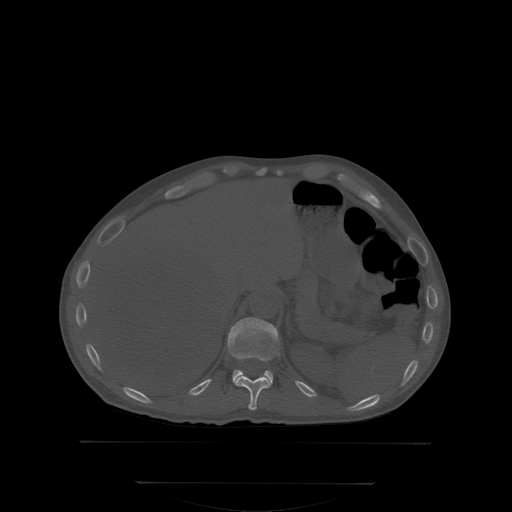
CT including the spine, one axial slice; slice 176 of 350 in the series (ordered by position); bone window (W 1800 / L 400 HU); 2.5 mm slice thickness; 512 × 512 image matrix, field of view 500 × 500 mm. Male patient, age 58 years. Case-level facts recorded for this patient, not image findings: primary cancer: prostate.
Outlined on this slice (semi-automatically segmented with operator editing):
- T11 vertebra: box from (x=229, y=346) to (x=278, y=410) px
- T12 vertebra: (x=229, y=318)–(x=279, y=386)